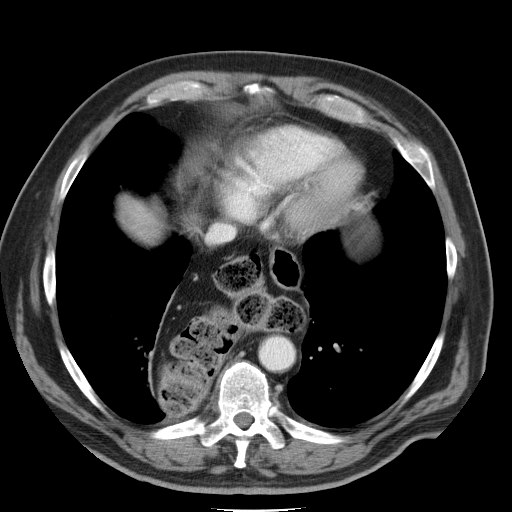
Contrast-enhanced abdominal CT, one axial slice; position 42 of 45 along the scan axis; 120 kVp; intravenous contrast given; soft-tissue window (W 400 / L 40 HU); 512 × 512 image matrix, field of view 386 × 386 mm. Male patient, age 65 years. Case-level facts recorded for this patient, not image findings: diagnosis: colorectal cancer liver metastases, imaged before liver resection; multiple liver metastases: yes; largest metastasis: 4.9 cm.
Annotated regions visible in this slice (outlined manually by an expert reader):
- liver: bounding box <123,201,158,238> (left, top, right, bottom; pixels)